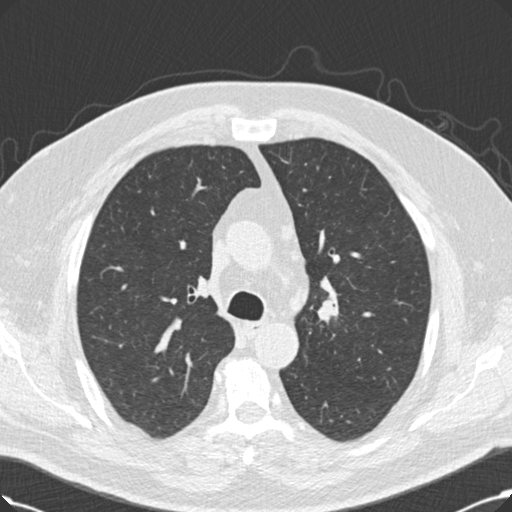
Low-dose screening chest CT, axial slice. Third screening round (two years after baseline). Lung window (W 1500 / L -600 HU). 2 mm slice thickness. Slice 63 of 214 in the series. 512 × 512 image matrix, field of view 365 × 365 mm. Male participant, aged 60 years at enrolment.
Expert reader's lesion annotation, bounding box [x1, y1, x2, y2] px = [317, 292, 348, 327]. Reader record for this screening exam (exam-level; its link to the box is not recorded): non-calcified nodule or mass ≥4 mm, left upper lobe, 20 × 20 mm, smooth margins, soft tissue attenuation, pre-existing on the prior screen: no. Official screen result: positive, other. Participant outcome: lung cancer diagnosed 53 days after this screen — squamous cell carcinoma, NOS, right upper lobe, 27 mm at pathology.